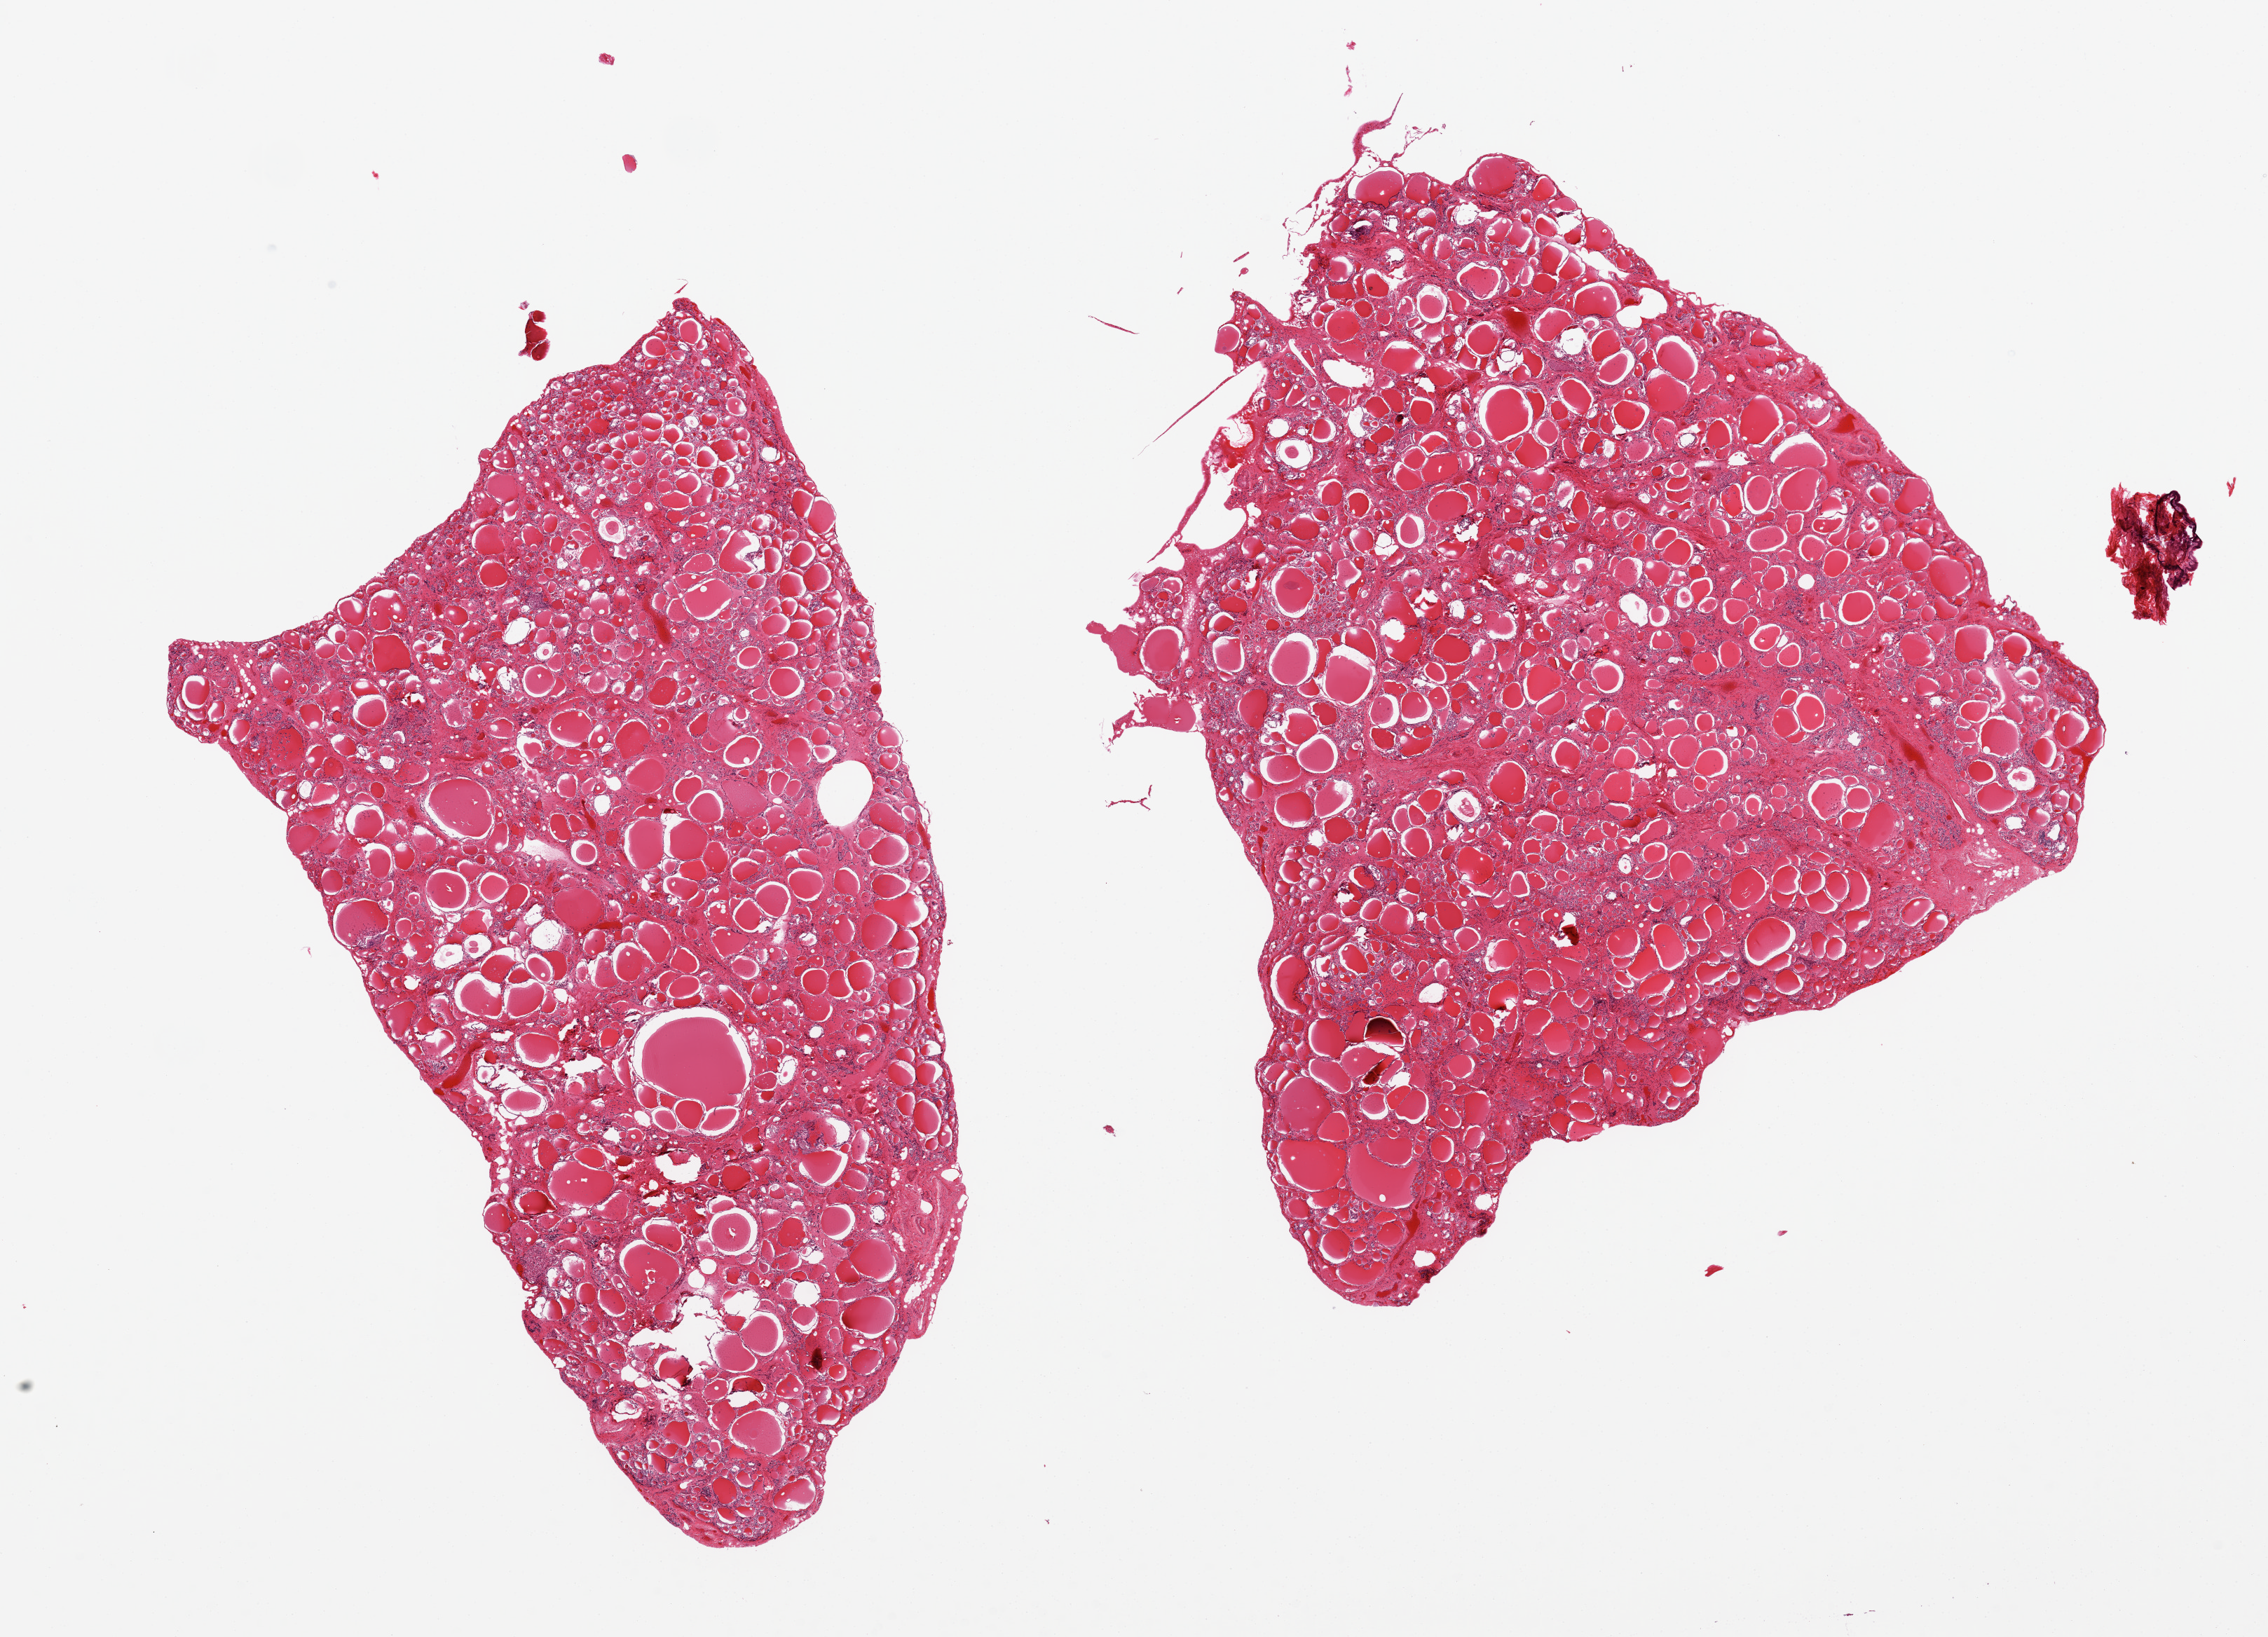
Digitized hematoxylin and eosin (H&E)-stained section, brightfield, low-resolution overview of the scanned area, about 25.6 x 18.5 mm; PAXgene-fixed, paraffin-embedded tissue; section of thyroid (target tissue); donor tissue sample. Donor: male.
Pathologist's review note for this sample: 2 pieces, nodular hyperplasia.